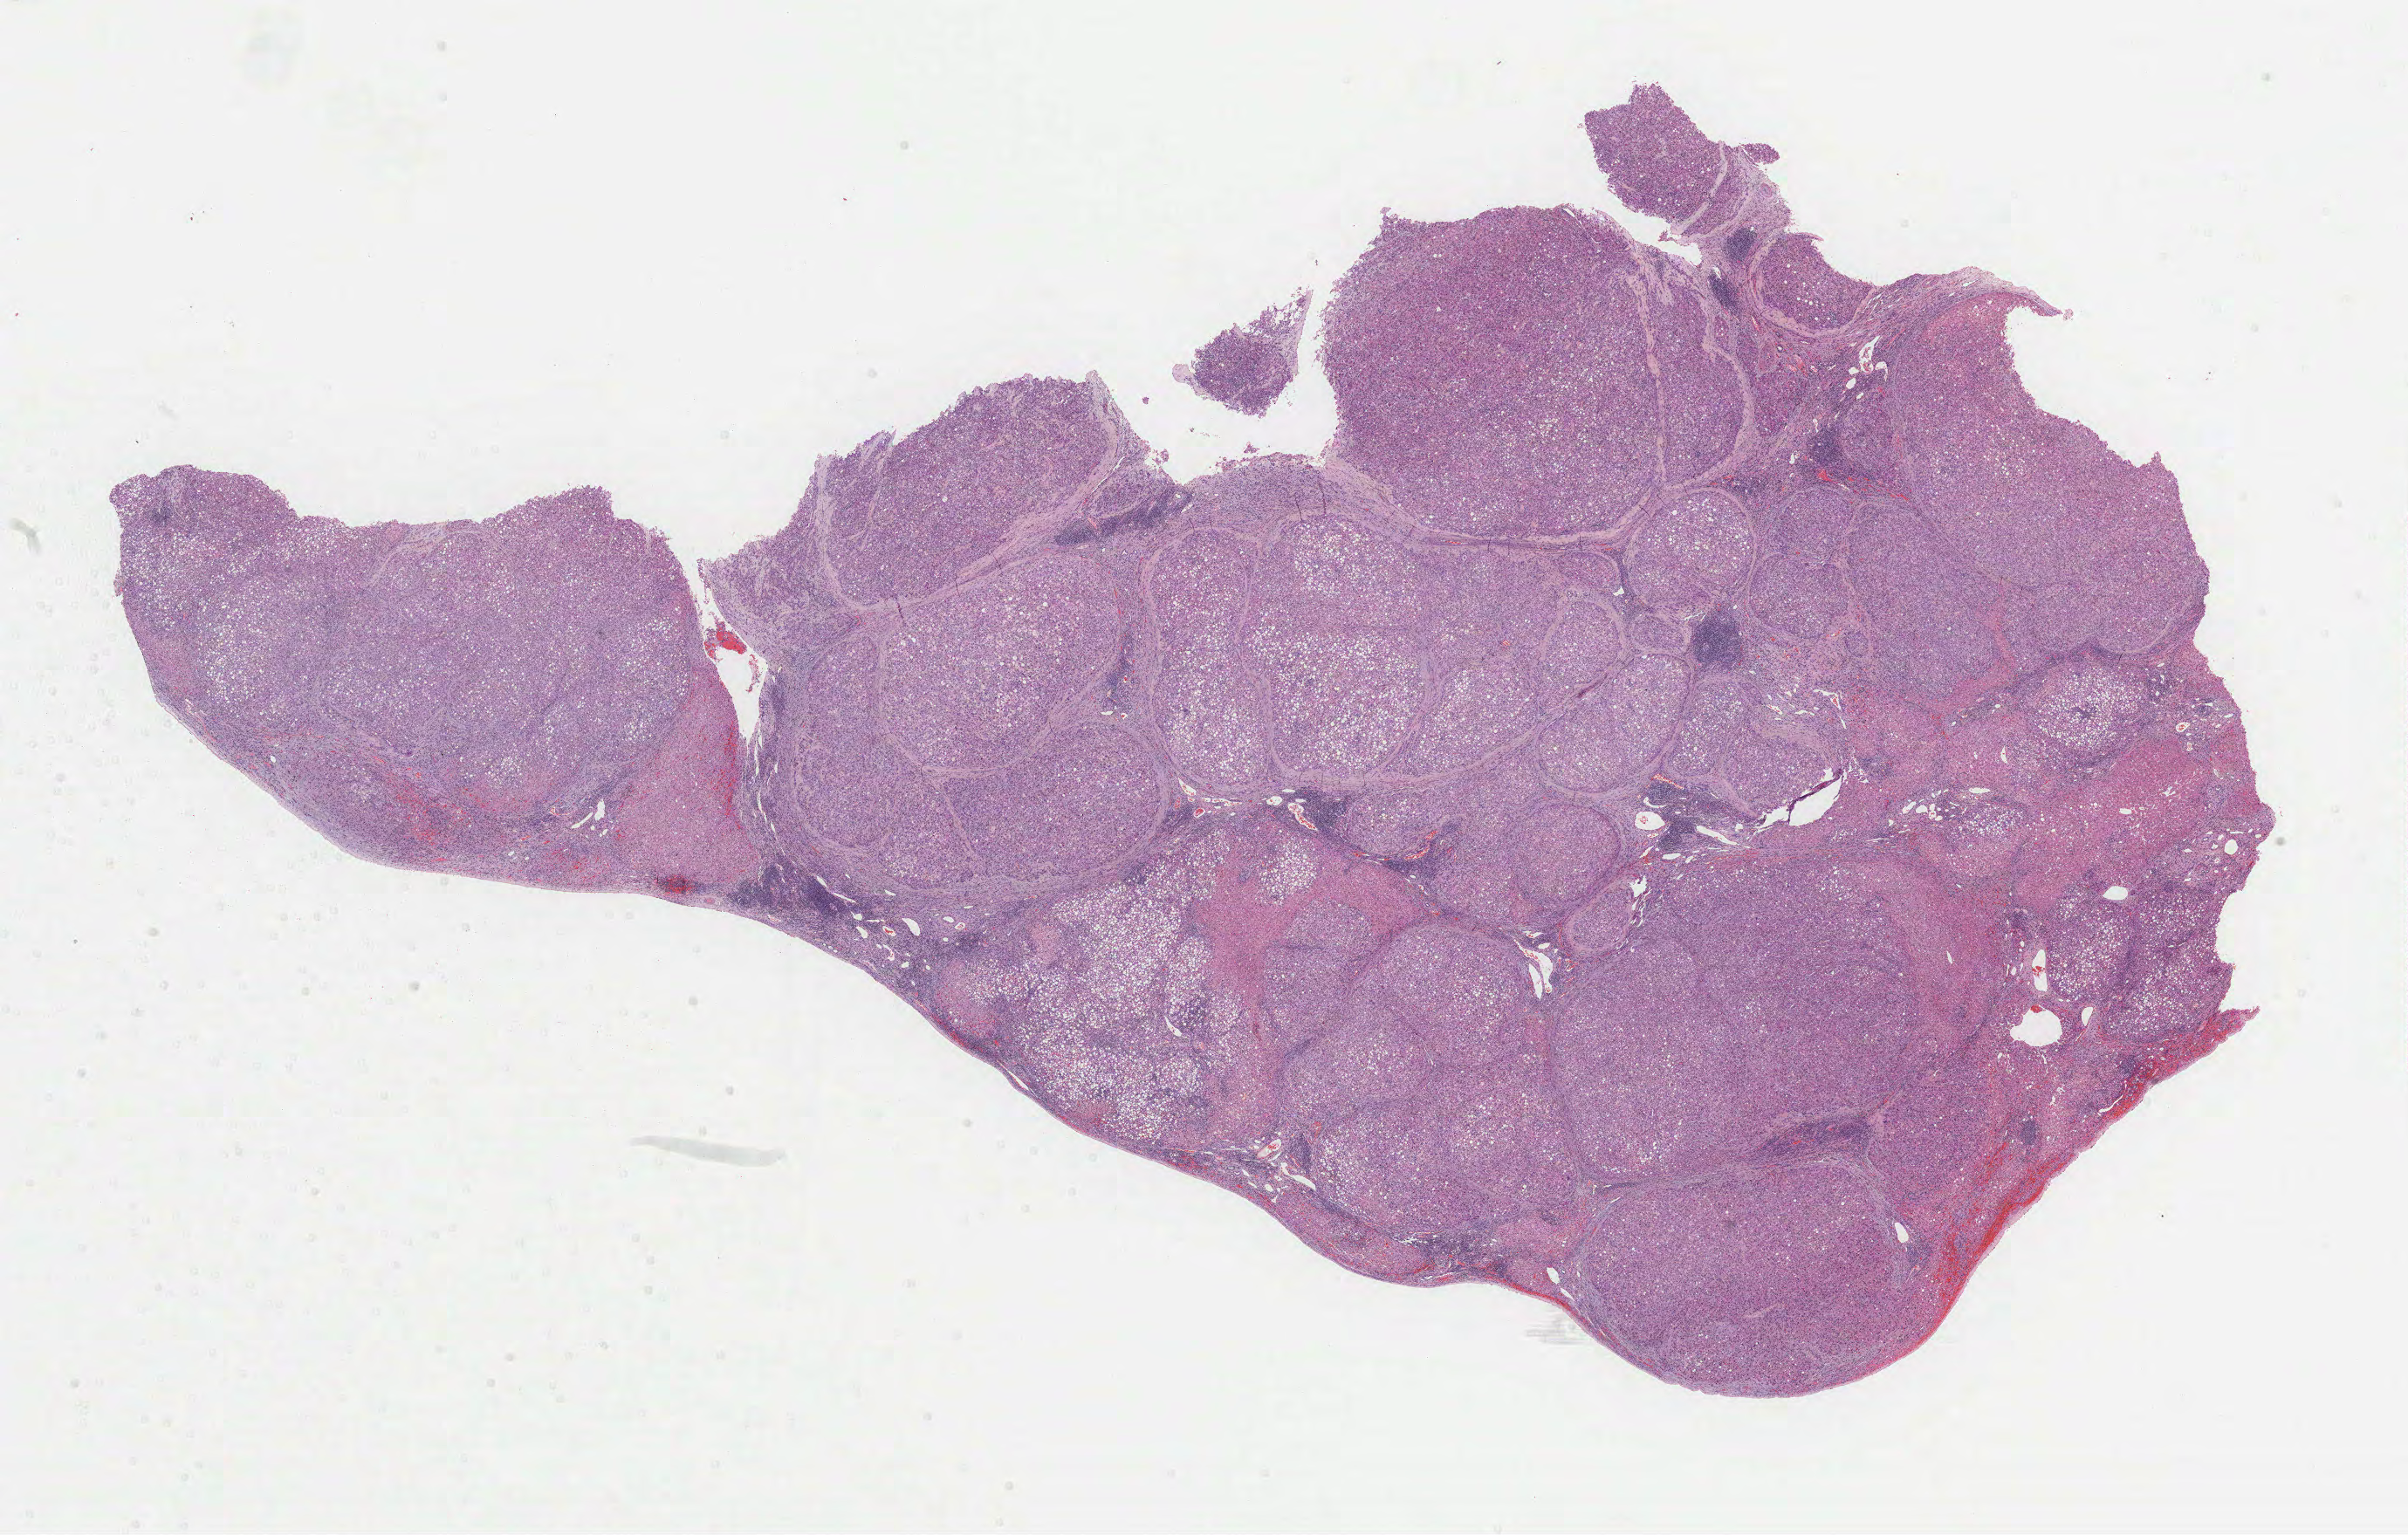
Whole-slide histology image, Hematoxylin and eosin (H&E) stained, shown as a low-resolution overview of the whole scanned area (about 22.3 x 14.2 mm), formalin-fixed paraffin-embedded (FFPE) diagnostic section, primary tumour sample from the liver. Male patient; age at initial diagnosis 64 years. Histologic grade: G2 (moderately differentiated).
Histologic diagnosis: Hepatocellular carcinoma, NOS. AJCC pathologic stage: I (6th edition).